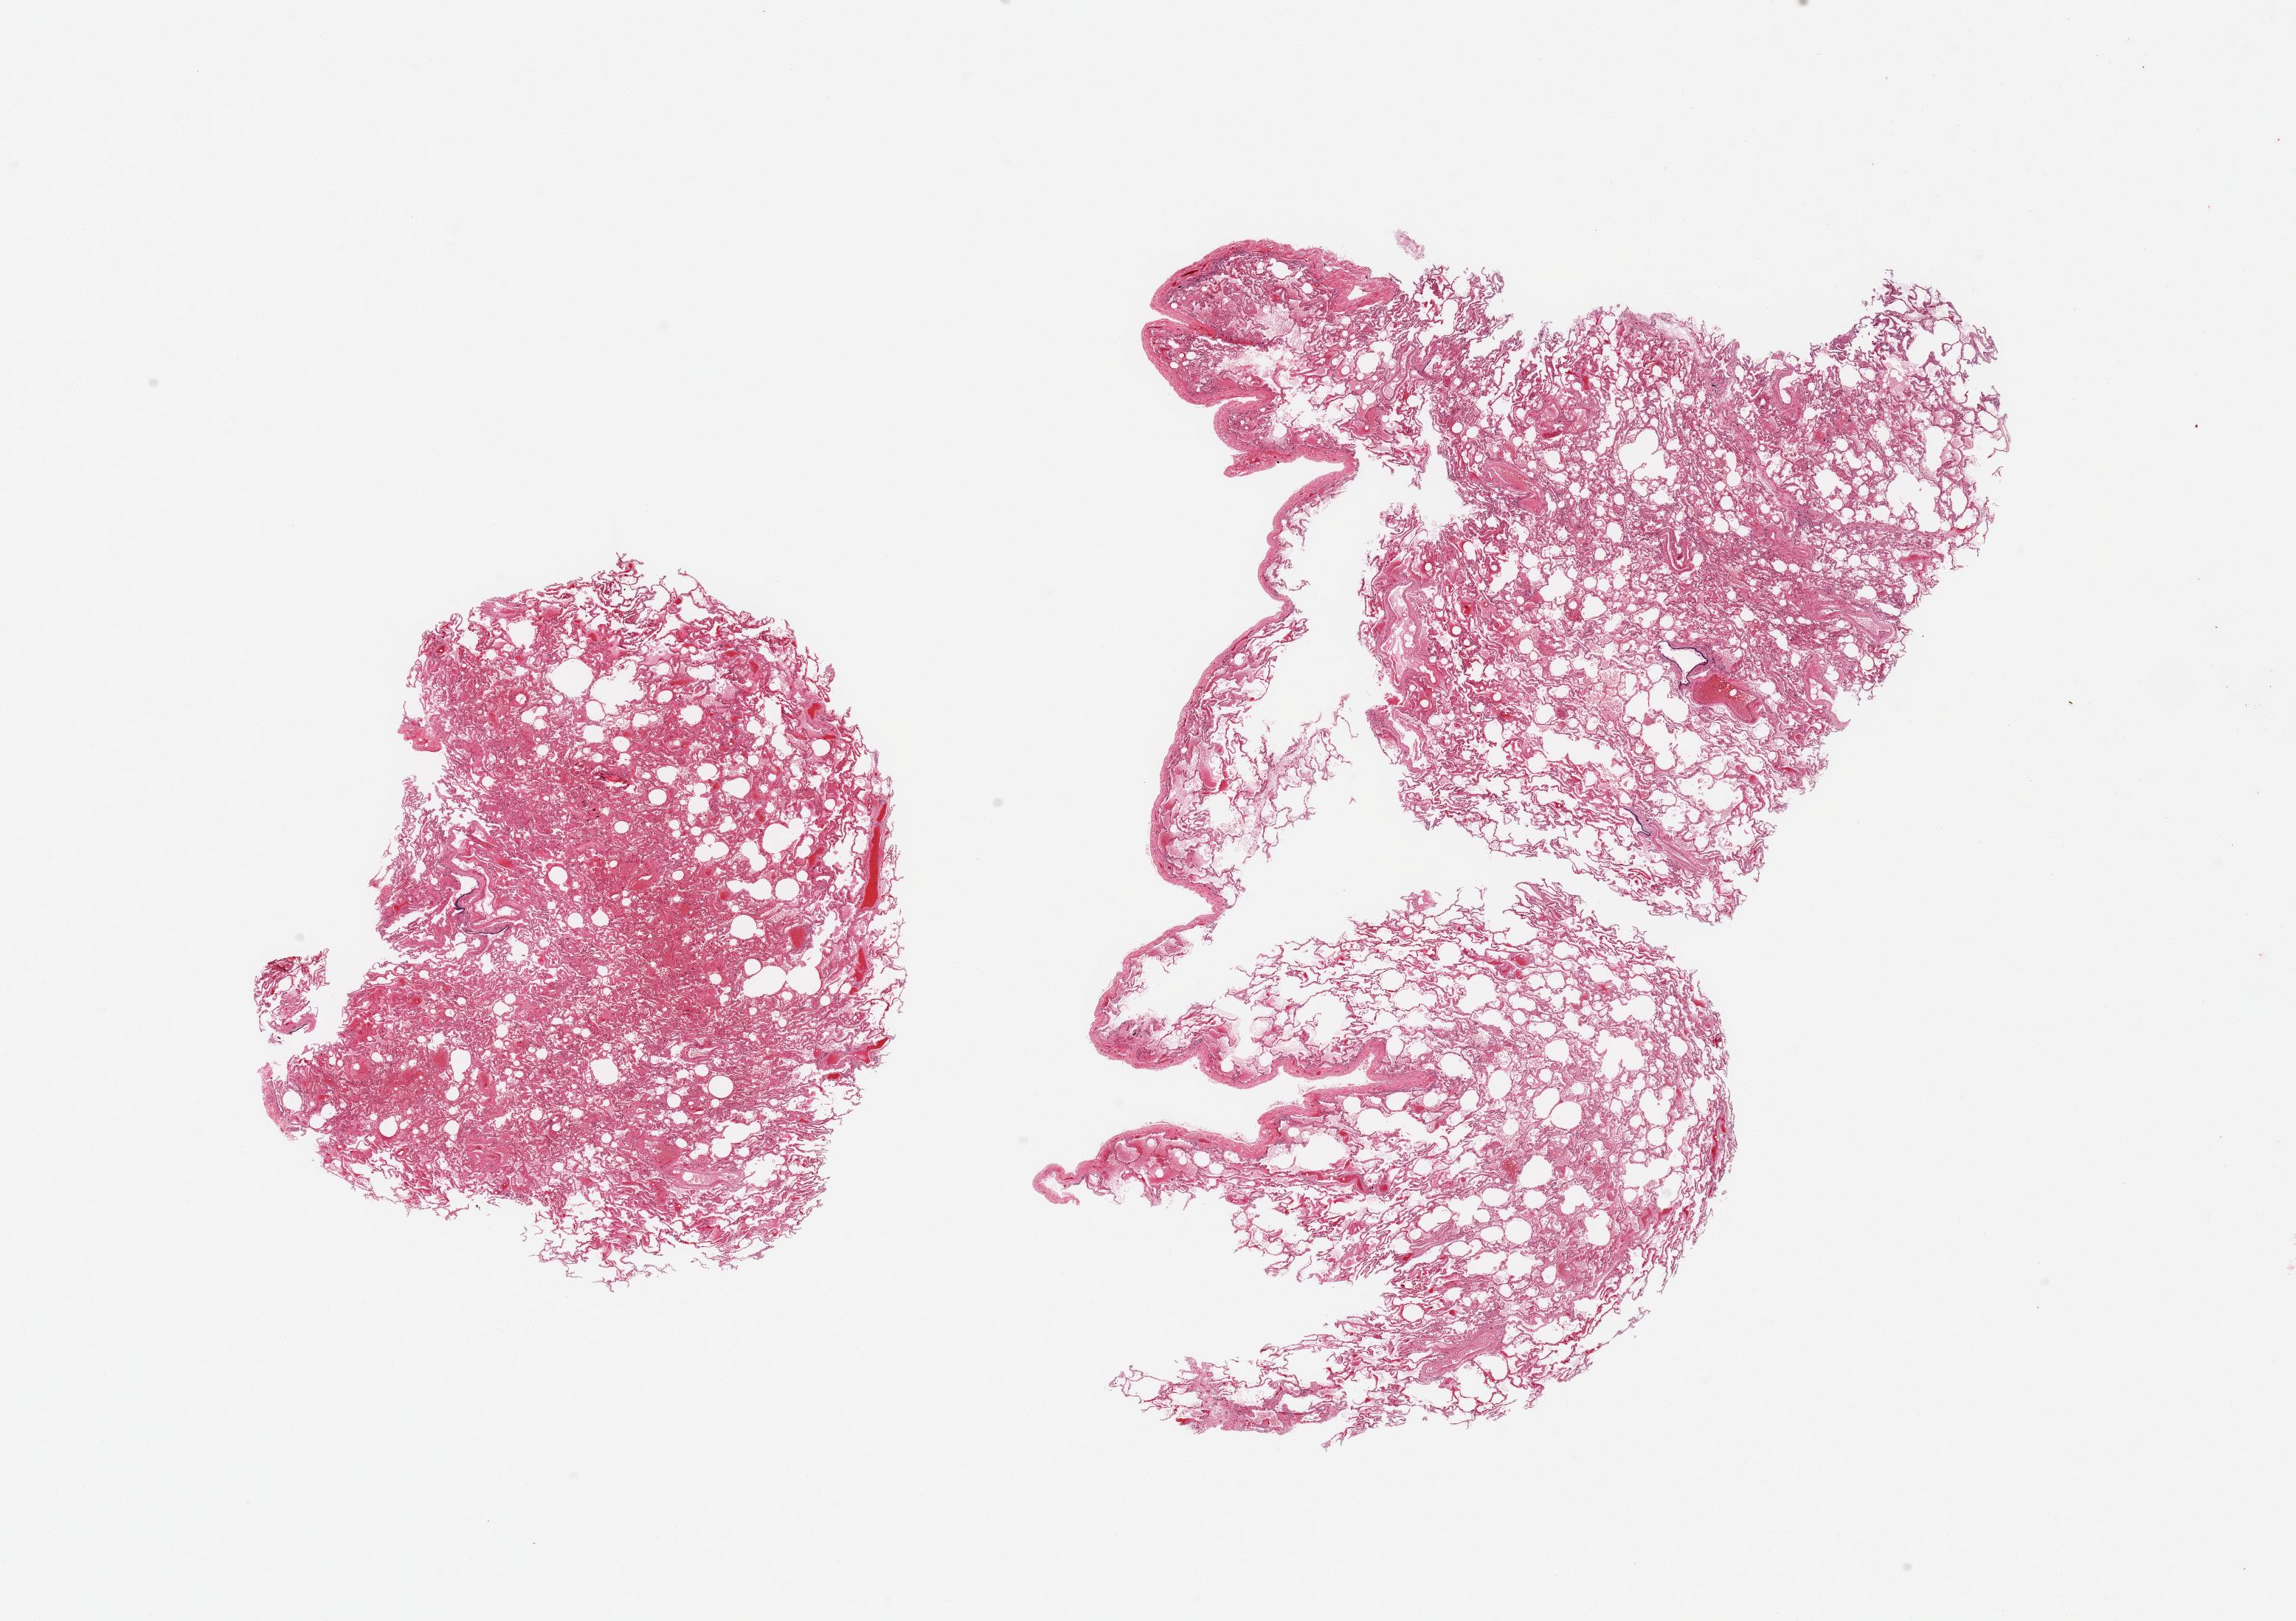
Digitized haematoxylin and eosin-stained section — whole scanned area (about 24.6 x 17.4 mm, acquisition: 20x scan) shown as a low-resolution overview; PAXgene-fixed, paraffin-embedded tissue; sampled site (target tissue): lung; donor tissue sample. Male donor.
Review note (as recorded): 2 pieces, moderate congestion.